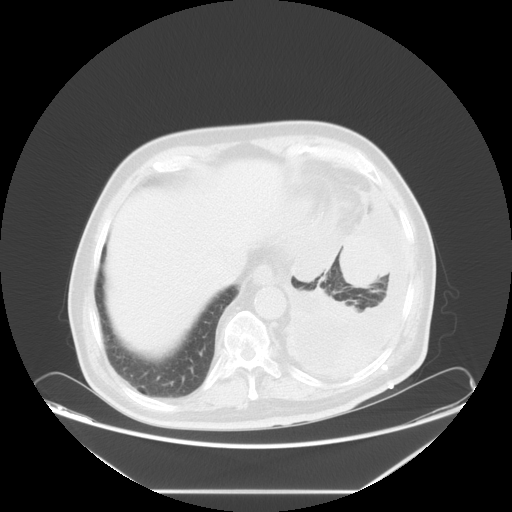
Chest CT, one axial slice; slice 16 of 63 in the series (ordered by position); 120 kVp; lung window (W 1500 / L -600 HU); 5 mm slice thickness; 512 × 512 image matrix, field of view 448 × 448 mm. Patient: male, 67 years. Case-level facts recorded for this patient, not image findings: clinical TNM (as recorded): T1b N1 M1a.
Annotated regions visible in this slice (bounding box drawn by a radiologist):
- lung tumour (recorded histology: small cell carcinoma): bounding box (x1, y1, x2, y2) in pixels: (337, 229, 391, 293)